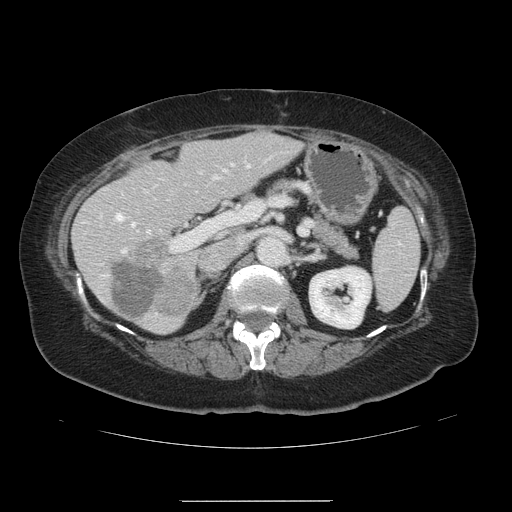
Contrast-enhanced abdominal CT, one axial slice; slice 67 of 141 in the series (ordered by position); intravenous contrast given; soft-tissue window (W 400 / L 40 HU); 2.5 mm slice thickness; 512 × 512 image matrix, field of view 393 × 393 mm. Female patient, age 74 years. Case-level facts recorded for this patient, not image findings: diagnosis: colorectal cancer liver metastases, imaged before liver resection; multiple liver metastases: yes; largest metastasis: 7 cm; chemotherapy before resection: no.
Outlined on this slice (expert manual segmentation):
- hepatic veins: box from (x=115, y=183) to (x=158, y=229) px
- liver: (x=73, y=132)–(x=299, y=333)
- planned liver remnant (the part of the liver to remain after resection): (x=73, y=132)–(x=299, y=333)
- portal vein (with intrahepatic branches): (x=99, y=163)–(x=249, y=253)
- liver metastasis: (x=112, y=262)–(x=164, y=322)
- liver metastasis: (x=132, y=239)–(x=194, y=315)